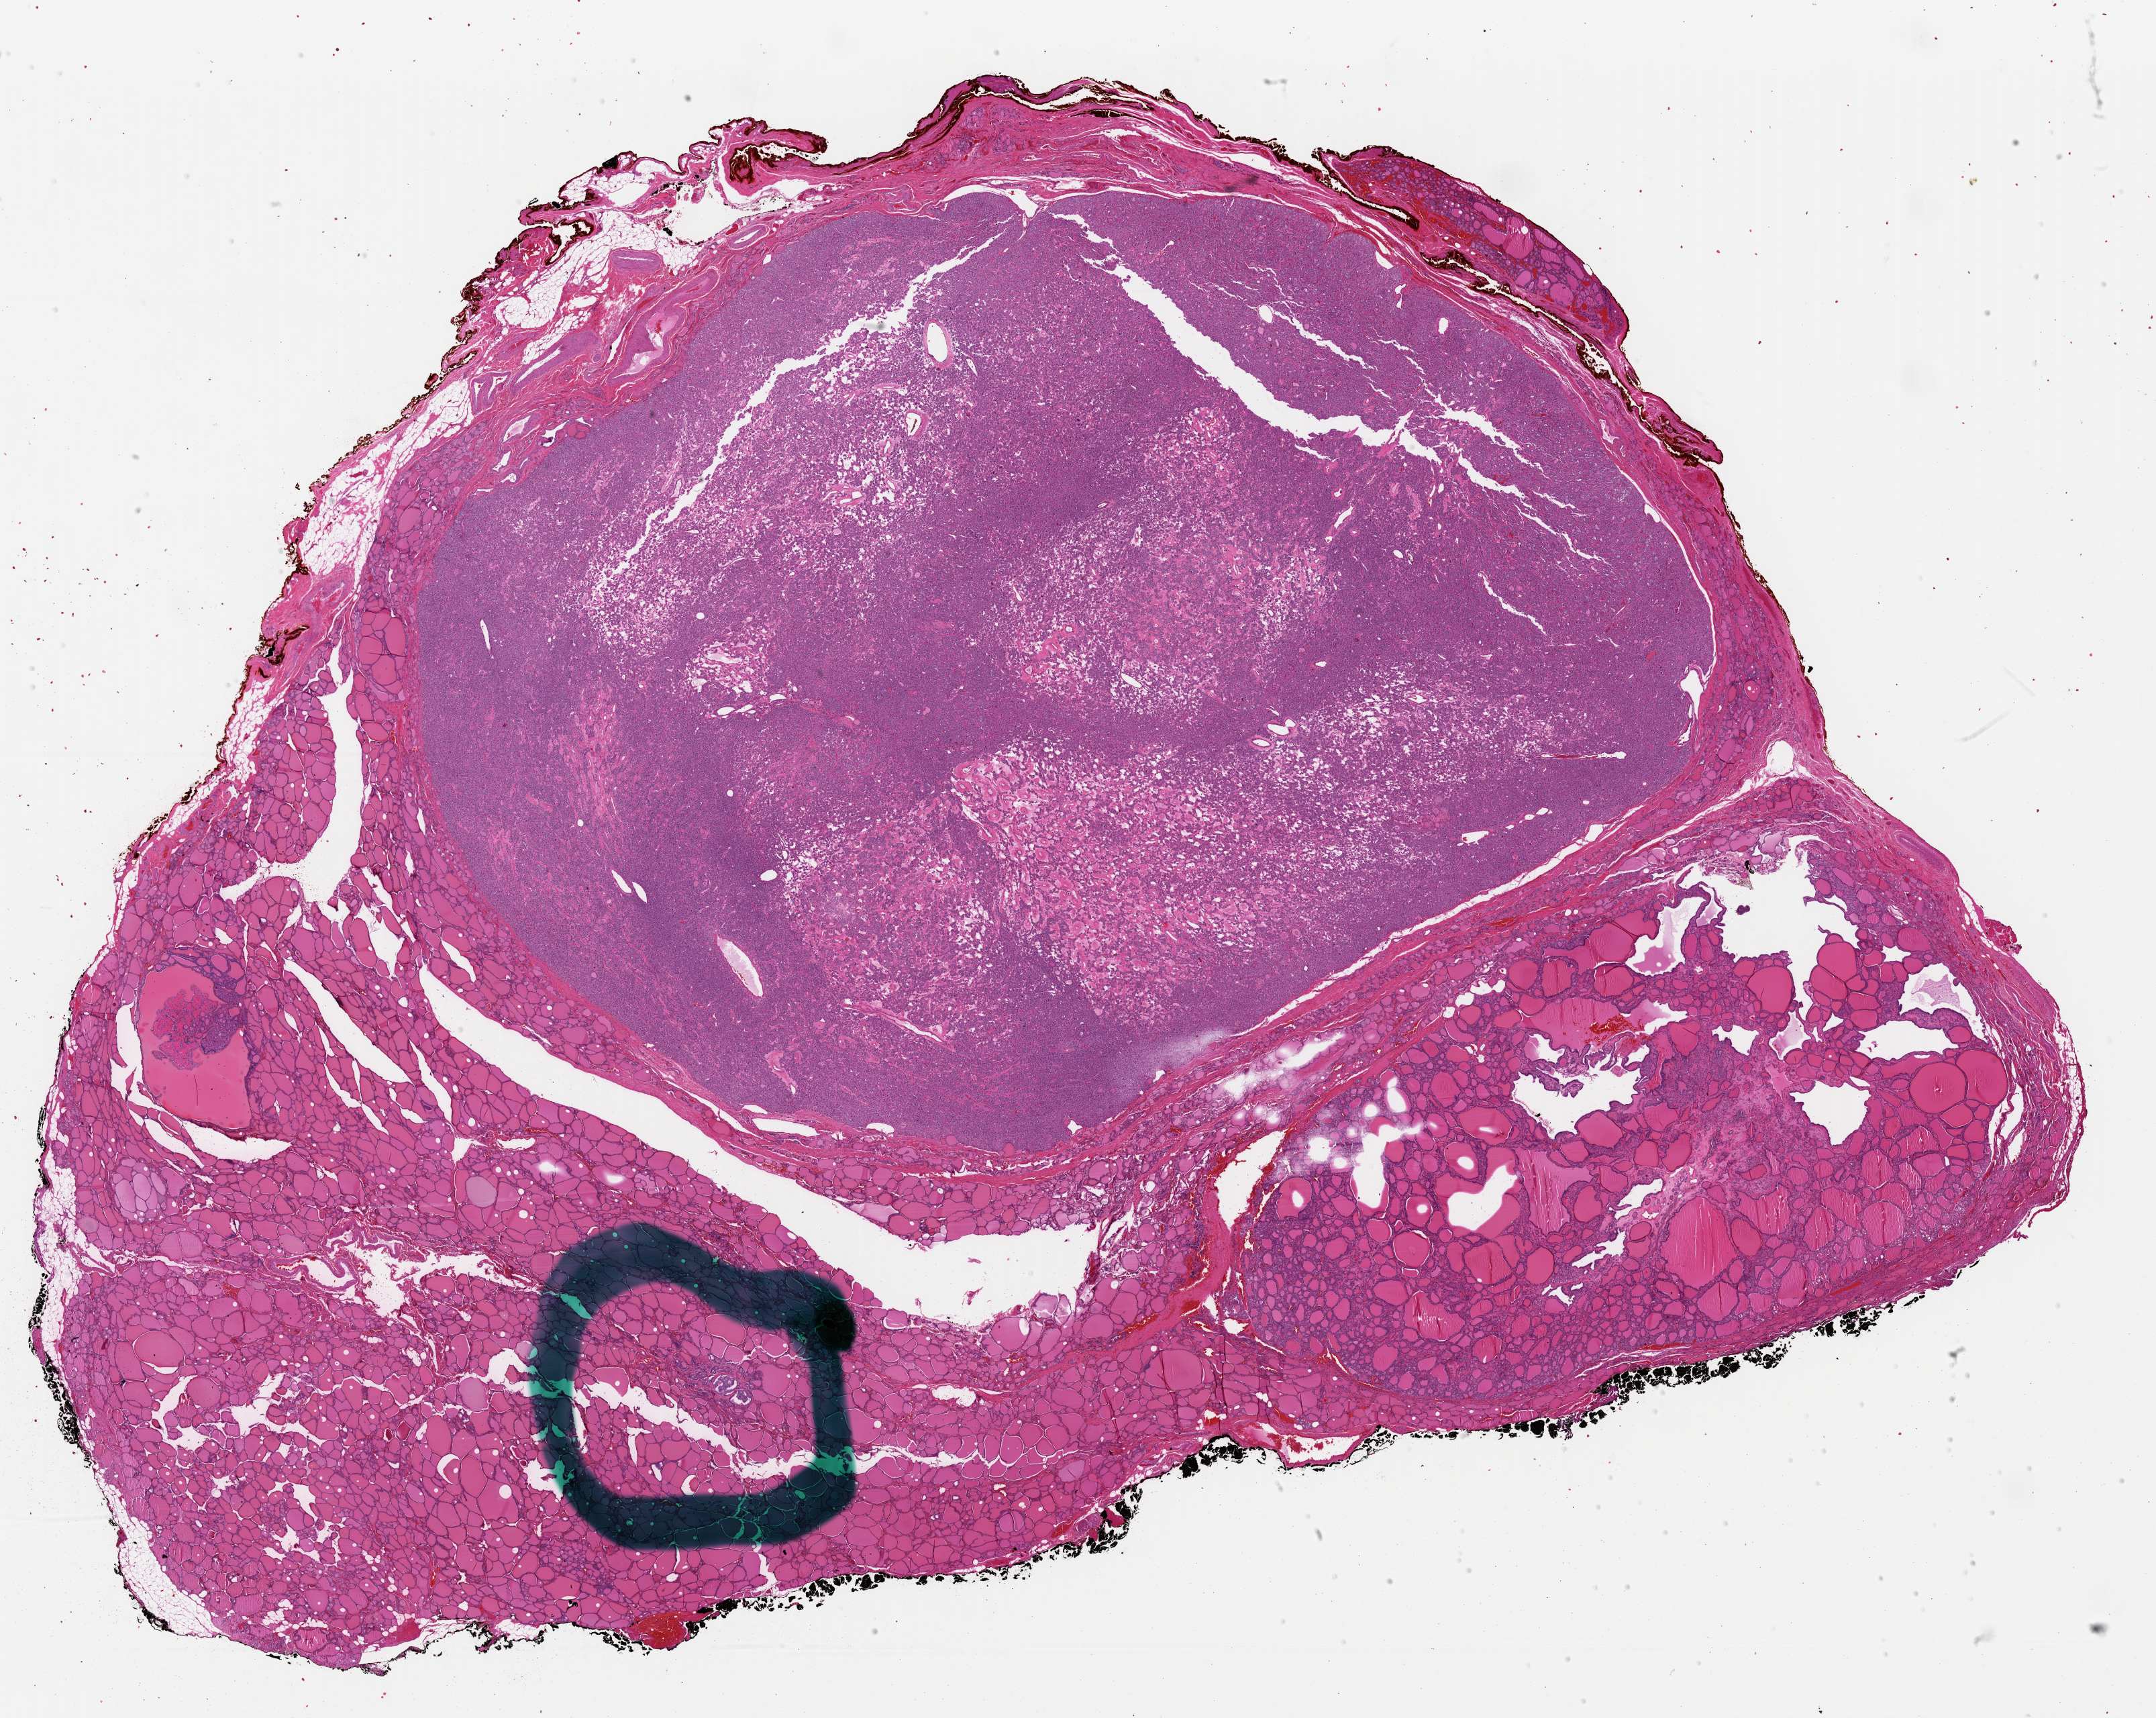
Digitized Hematoxylin and eosin (H&E) stained tissue section (whole slide), low-resolution overview of the scanned area, about 25.4 x 20.2 mm; FFPE section; thyroid, primary tumour sample. Female, age 61 years at initial diagnosis.
Histologic diagnosis: Papillary adenocarcinoma, NOS (thyroid gland). AJCC pathologic stage: I (6th edition).